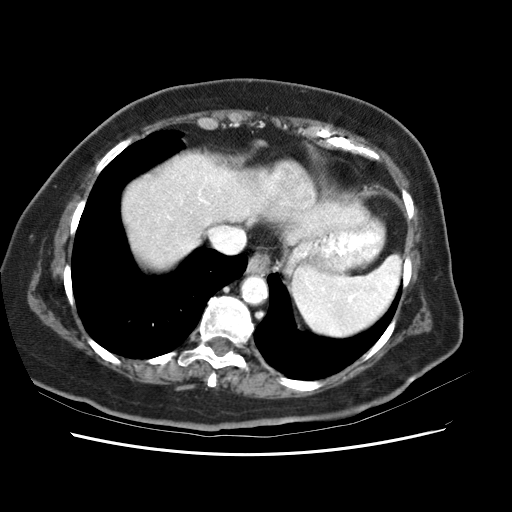
Contrast-enhanced abdominal CT (liver protocol), one axial slice. Position 55 of 62 along the scan axis. Soft-tissue window (W 400 / L 40 HU). 512 × 512 image matrix, field of view 340 × 340 mm. Case-level facts recorded for this patient, not image findings: diagnosis: hepatocellular carcinoma (patient treated with transarterial chemoembolisation; whether this scan precedes or follows treatment is not stated here); TNM stage (as recorded): Stage-I; Child-Pugh class: B; tumour size: 5.3 cm.
Annotated regions visible in this slice (semi-automatic segmentation, software-assisted and operator-edited):
- abdominal aorta: bounding box <242,277,266,305> (left, top, right, bottom; pixels)
- liver parenchyma outside the tumour (the mass and vessels are separate outlines, so this box may not span the whole liver): <128,164,242,247>
- mass: <289,182,312,205>
- liver vessels: <174,213,180,218>